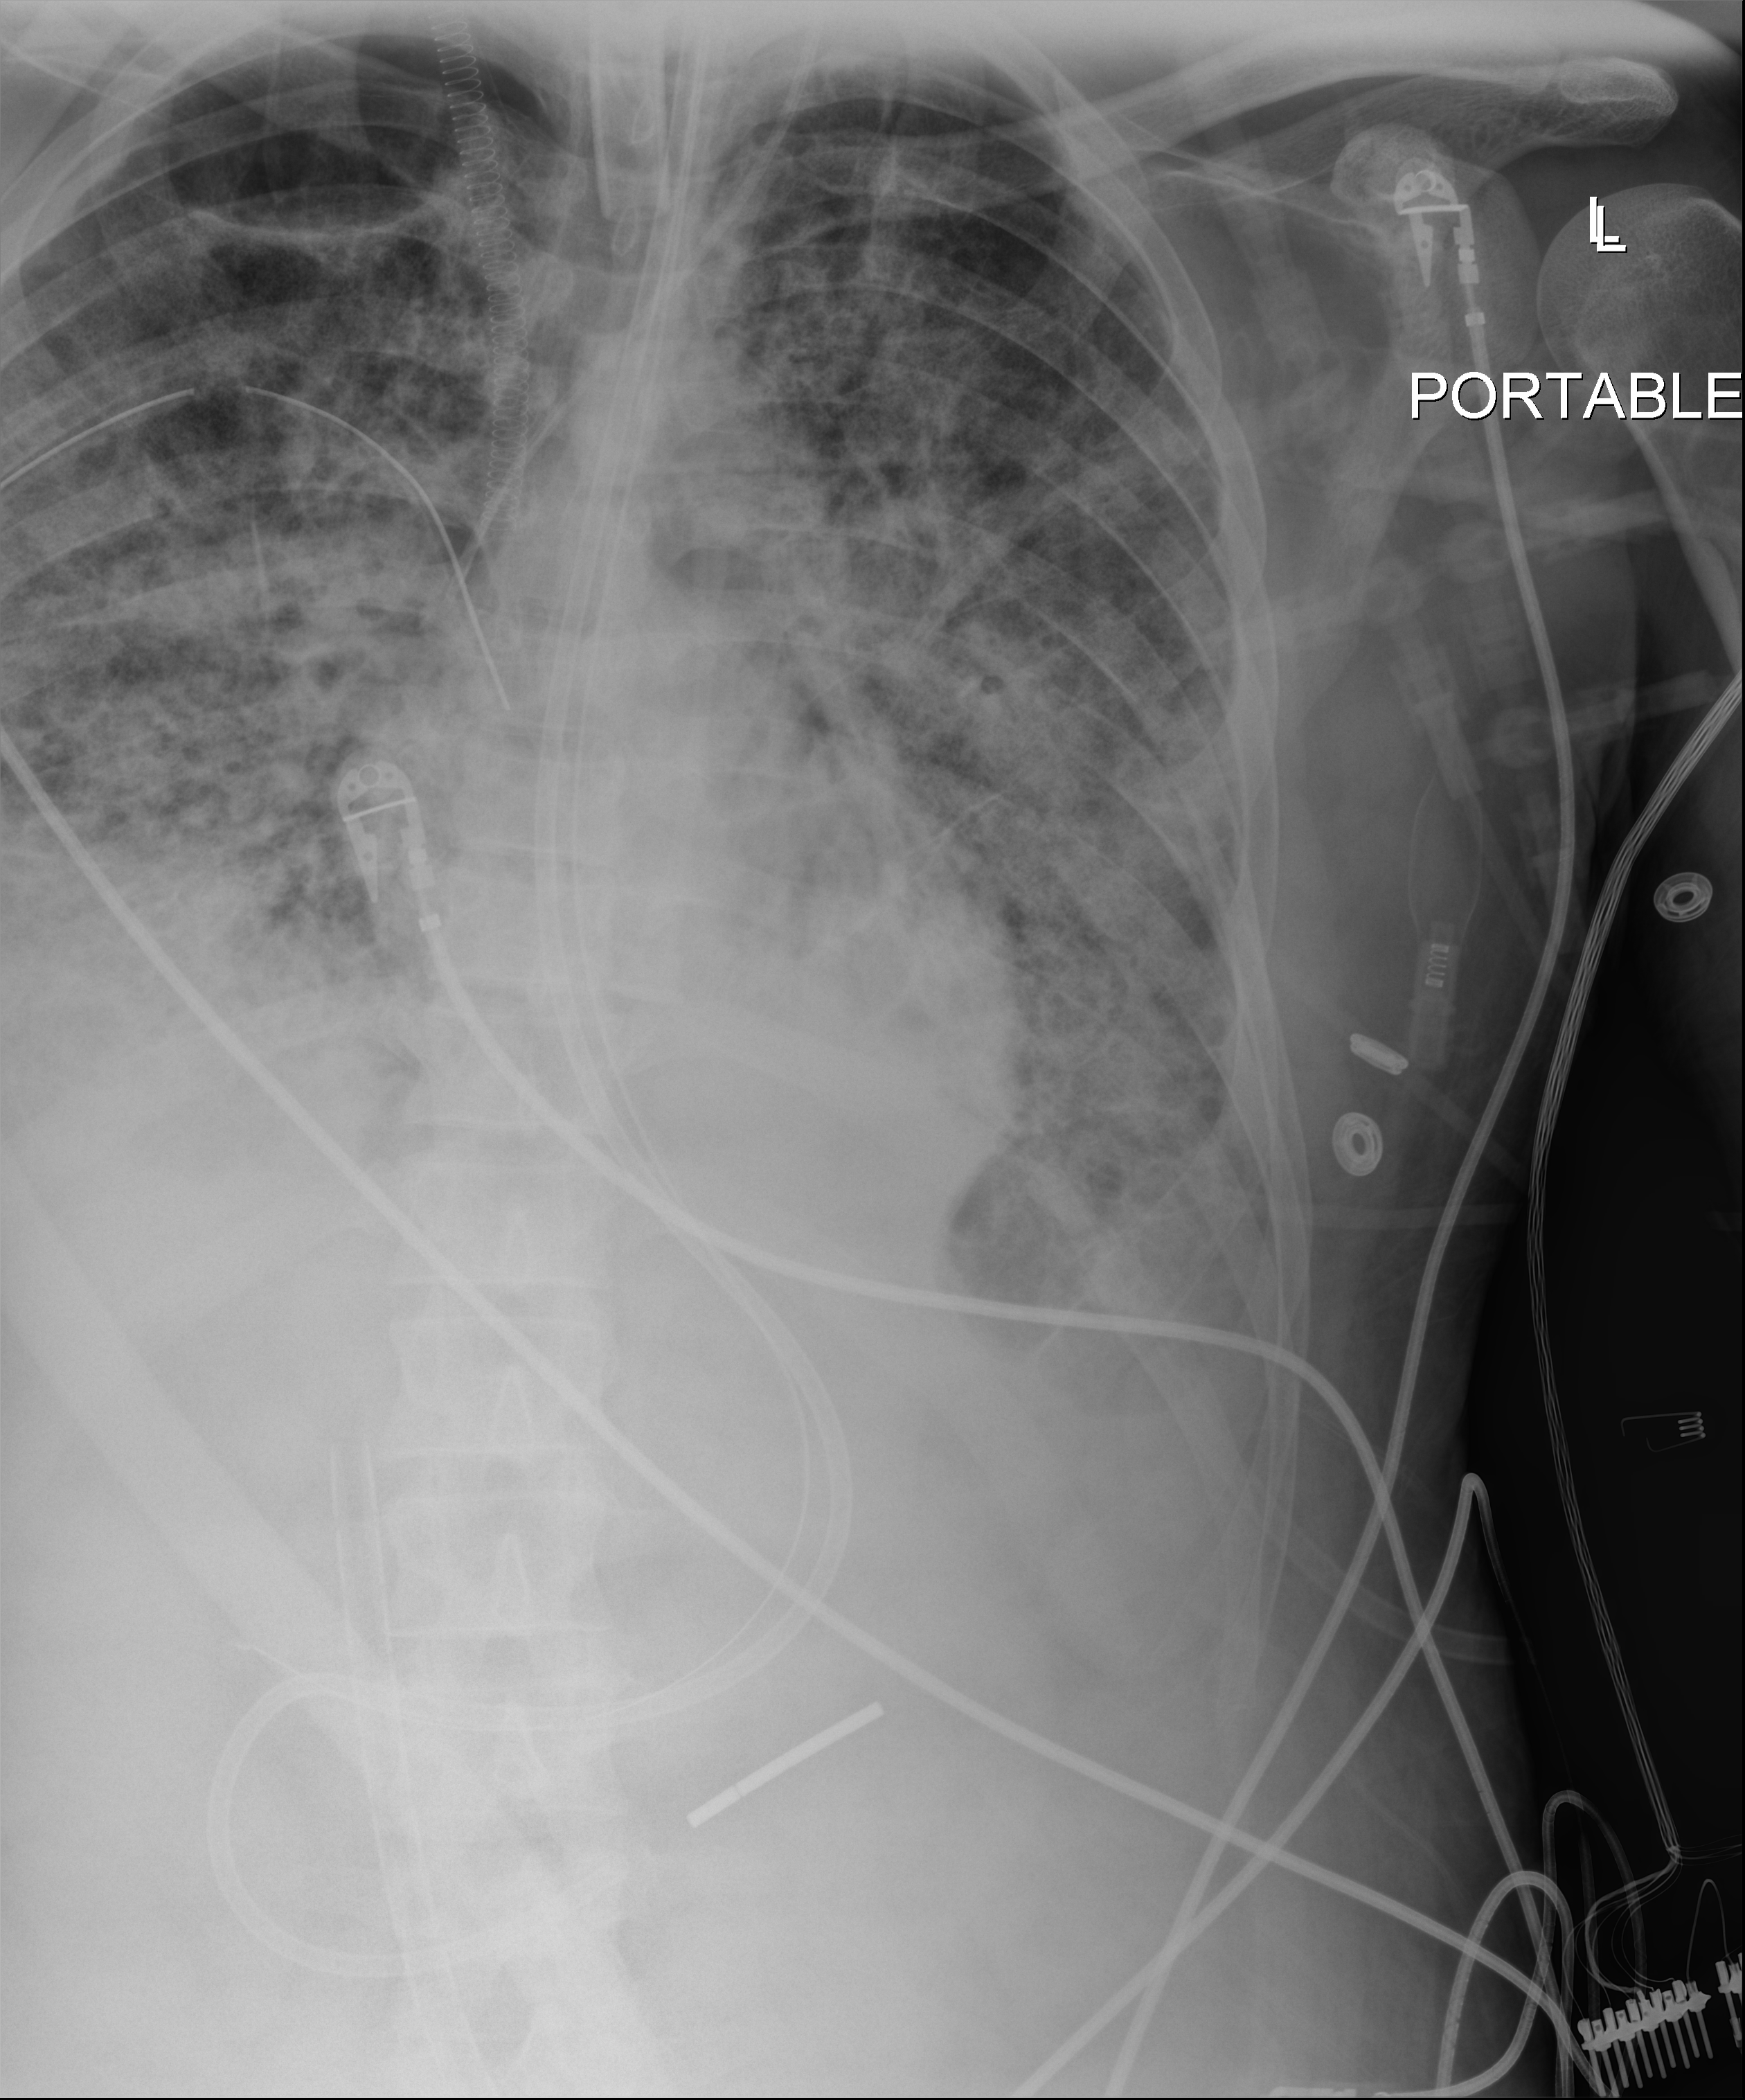
Abdomen X-ray (portable), anteroposterior (AP) projection. Adult patient hospitalised with COVID-19, age 18–59 years.
From the hospital-stay record, not from the radiograph (when in the stay this image was taken is not recorded): chronic kidney disease (admission record): no.